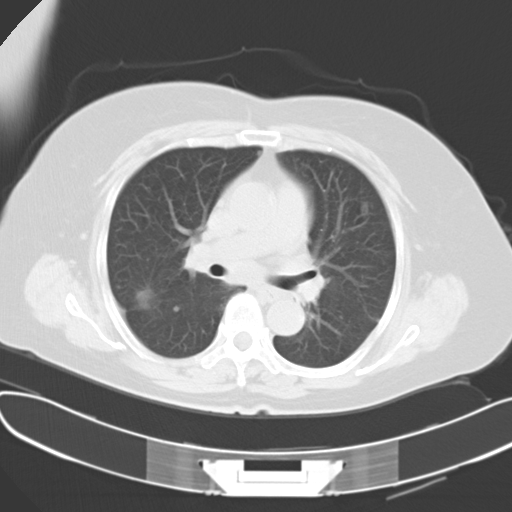
Chest CT, one axial slice; slice 21 of 30 in the series (ordered by position); reconstruction kernel B40f; lung window (W 1500 / L -600 HU); 10 mm slice thickness; 512 × 512 image matrix. Female patient, age 63 years. From the clinical record (not read from this slice): clinical TNM (as recorded): T1c N3 M1a.
Outlined on this slice (bounding box drawn by a radiologist):
- lung tumour (recorded histology: adenocarcinoma): bounding box <130,280,158,313> (left, top, right, bottom; pixels)